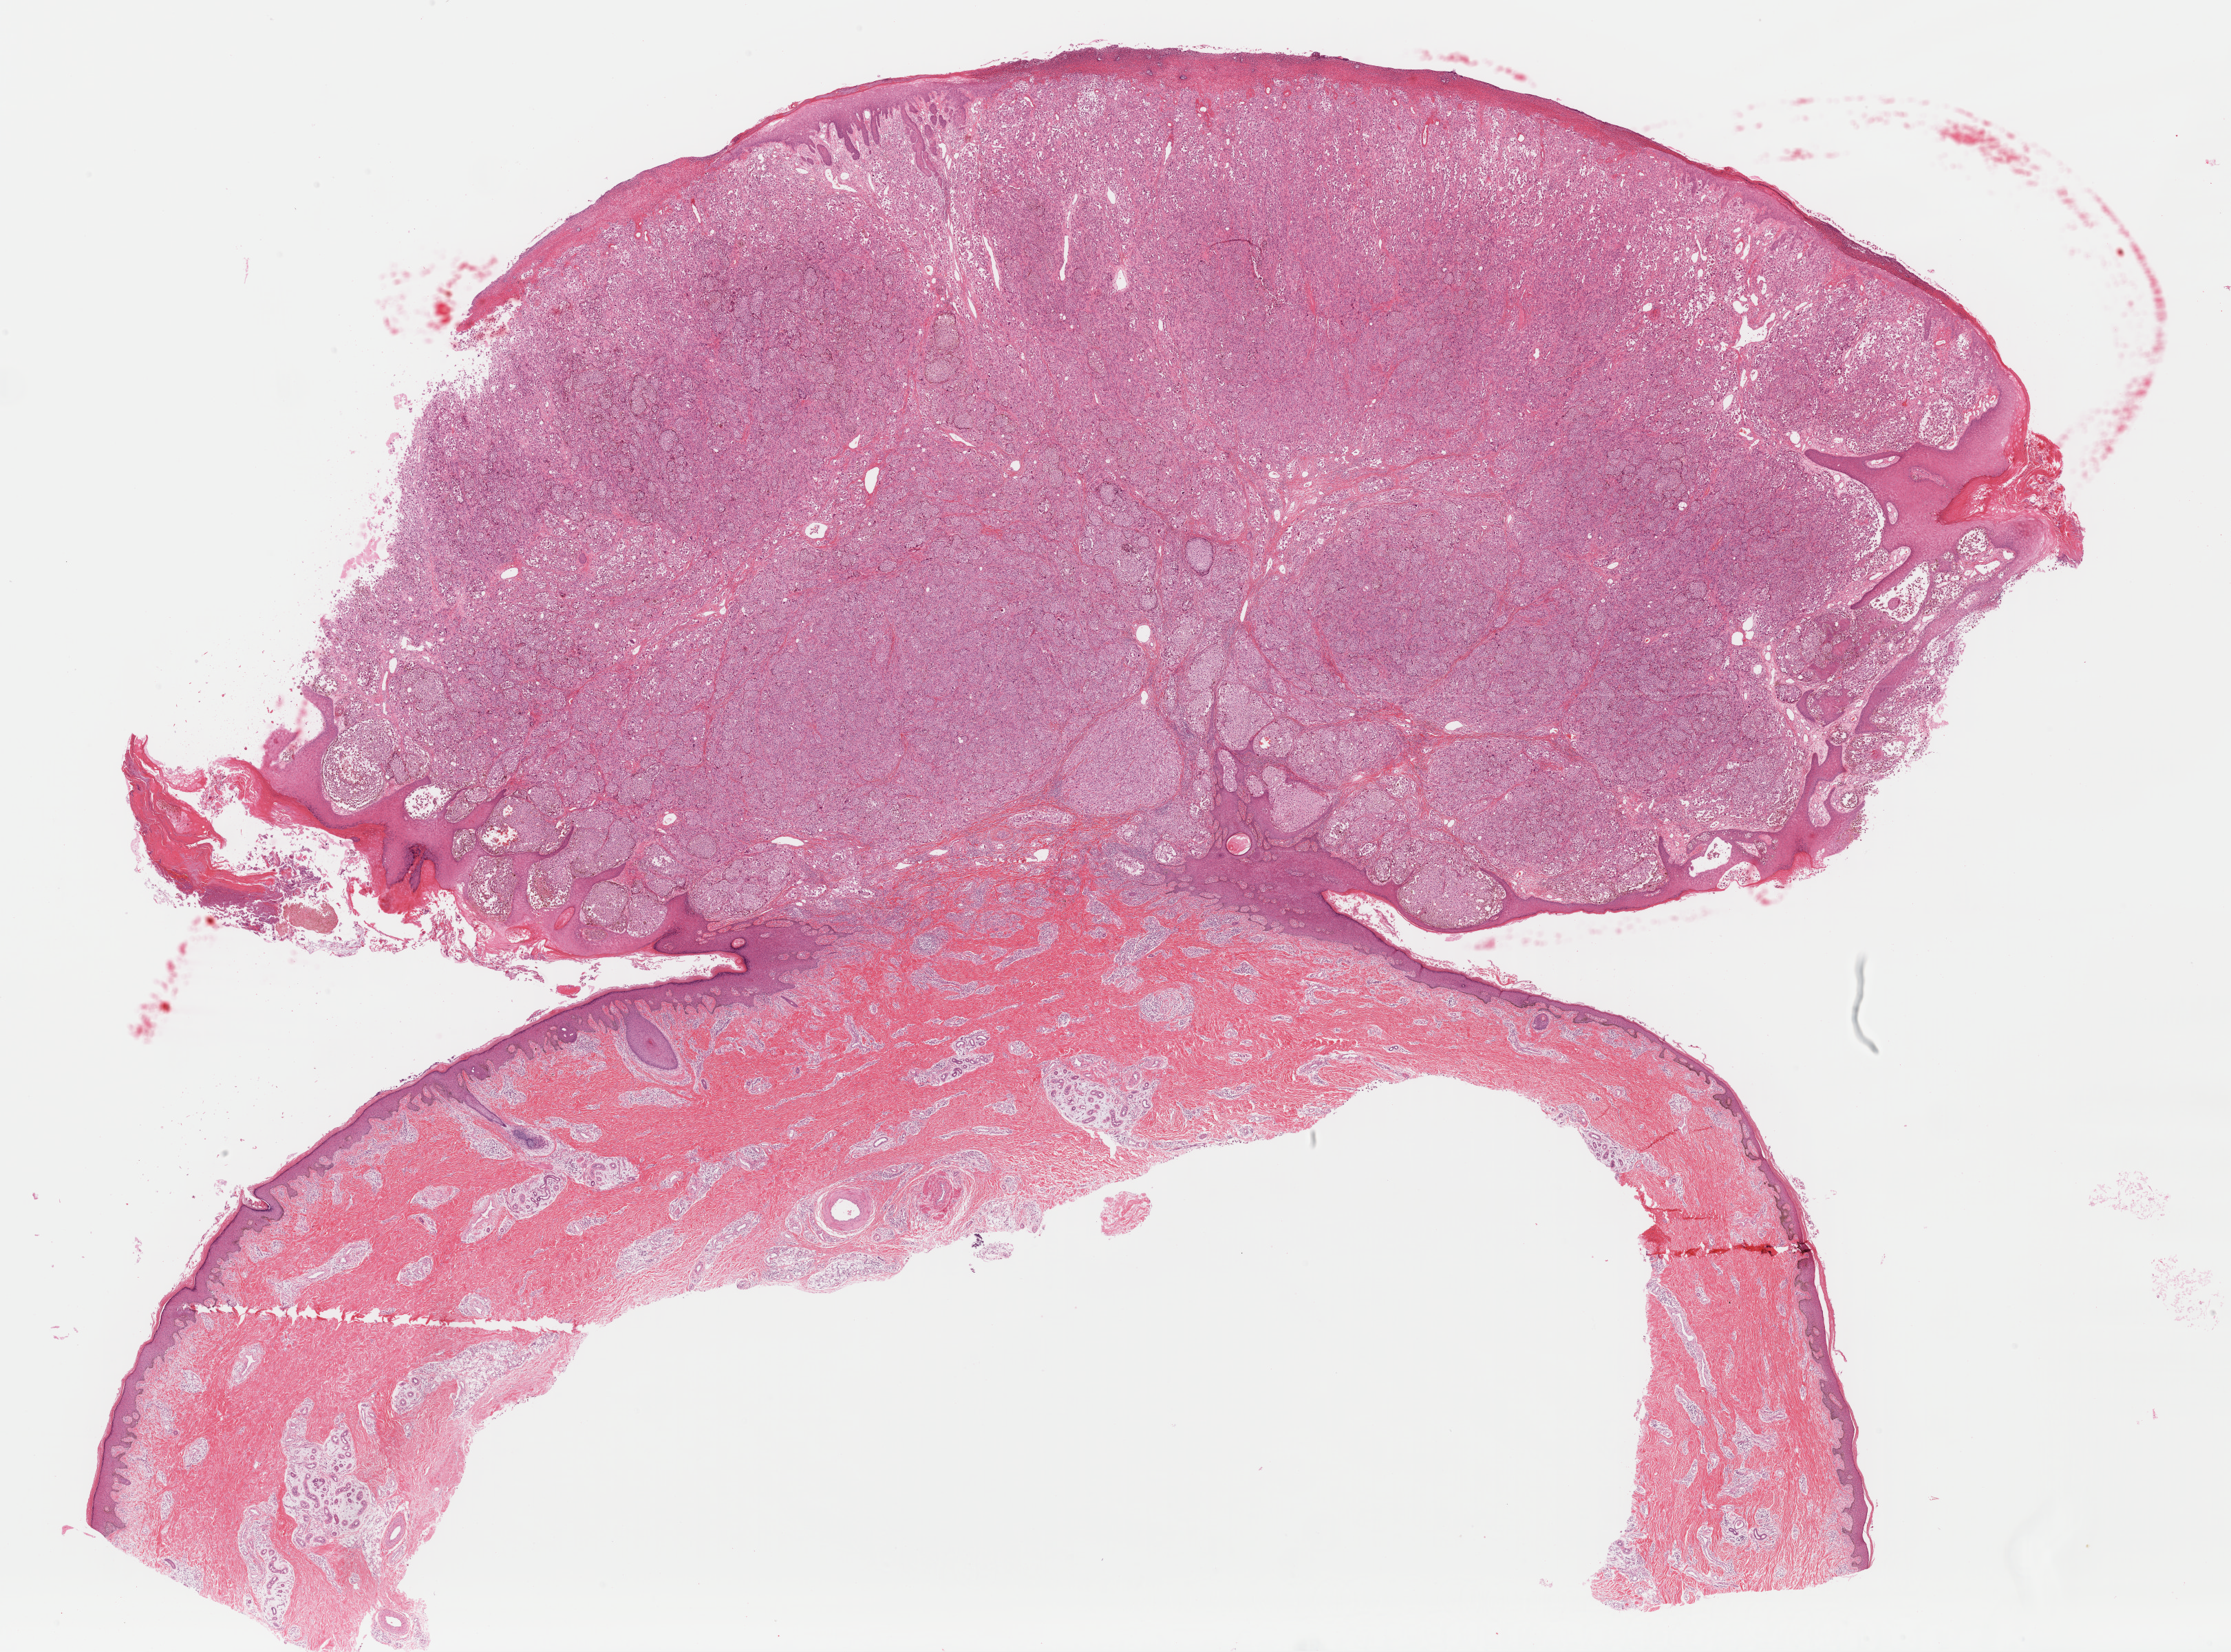
Hematoxylin and eosin (H&E) stained whole-slide image, whole scanned area (about 25.6 x 19.0 mm, from a 40x scan) shown as a low-resolution overview; formalin-fixed paraffin-embedded (FFPE) diagnostic section; sample: primary tumour, skin. Patient: male, age at initial diagnosis 49 years.
- AJCC pathologic stage: IIIC (7th edition)
- diagnosis: Malignant melanoma, NOS